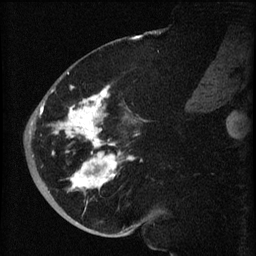
Breast MRI (dynamic contrast-enhanced), one sagittal slice; dynamic contrast-enhanced series, image 2 of 3 at this slice position (ordered by acquisition); 1.5 T; TE 4.2 ms, TR 8.2 ms; 256 × 256 image matrix. Female patient, age 71 years.
Structures marked on this image (semi-automatically segmented with operator editing):
- analysis volume of interest (the breast-tissue region the enhancement analysis was run in; not a lesion): bounding box (x1, y1, x2, y2) in pixels: (40, 72, 140, 196)
- tumour enhancement mask (voxels above the 70 % enhancement threshold inside the analysis volume of interest): (40, 72, 137, 191)